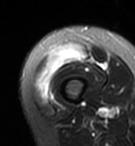
MRI of an extremity soft-tissue mass, one axial slice. T2-weighted fat-saturated. MR volume resampled by the dataset authors to the PET/CT grid (not the native acquisition matrix). 3.27 mm slice thickness. 135 × 146 image matrix, field of view 132 × 143 mm. Female patient. Case-level facts recorded for this patient, not image findings: histological type: pleiomorphic undifferentiated sarcoma; grade: high; site of the primary tumour: right quadricep.
Annotated regions visible in this slice (expert contour drawn on MRI and transferred to this co-registered scan by the dataset authors):
- gross tumour volume including surrounding oedema: bounding box [x1, y1, x2, y2] px = [35, 45, 86, 98]